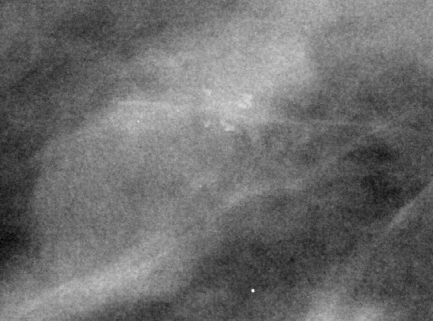
Region of interest cut from a scanned film mammogram (one marked finding), right breast, CC view.
- Calcifications, morphology pleomorphic, distribution clustered; BI-RADS assessment category 4; pathology result (as recorded, not read from the image): benign.